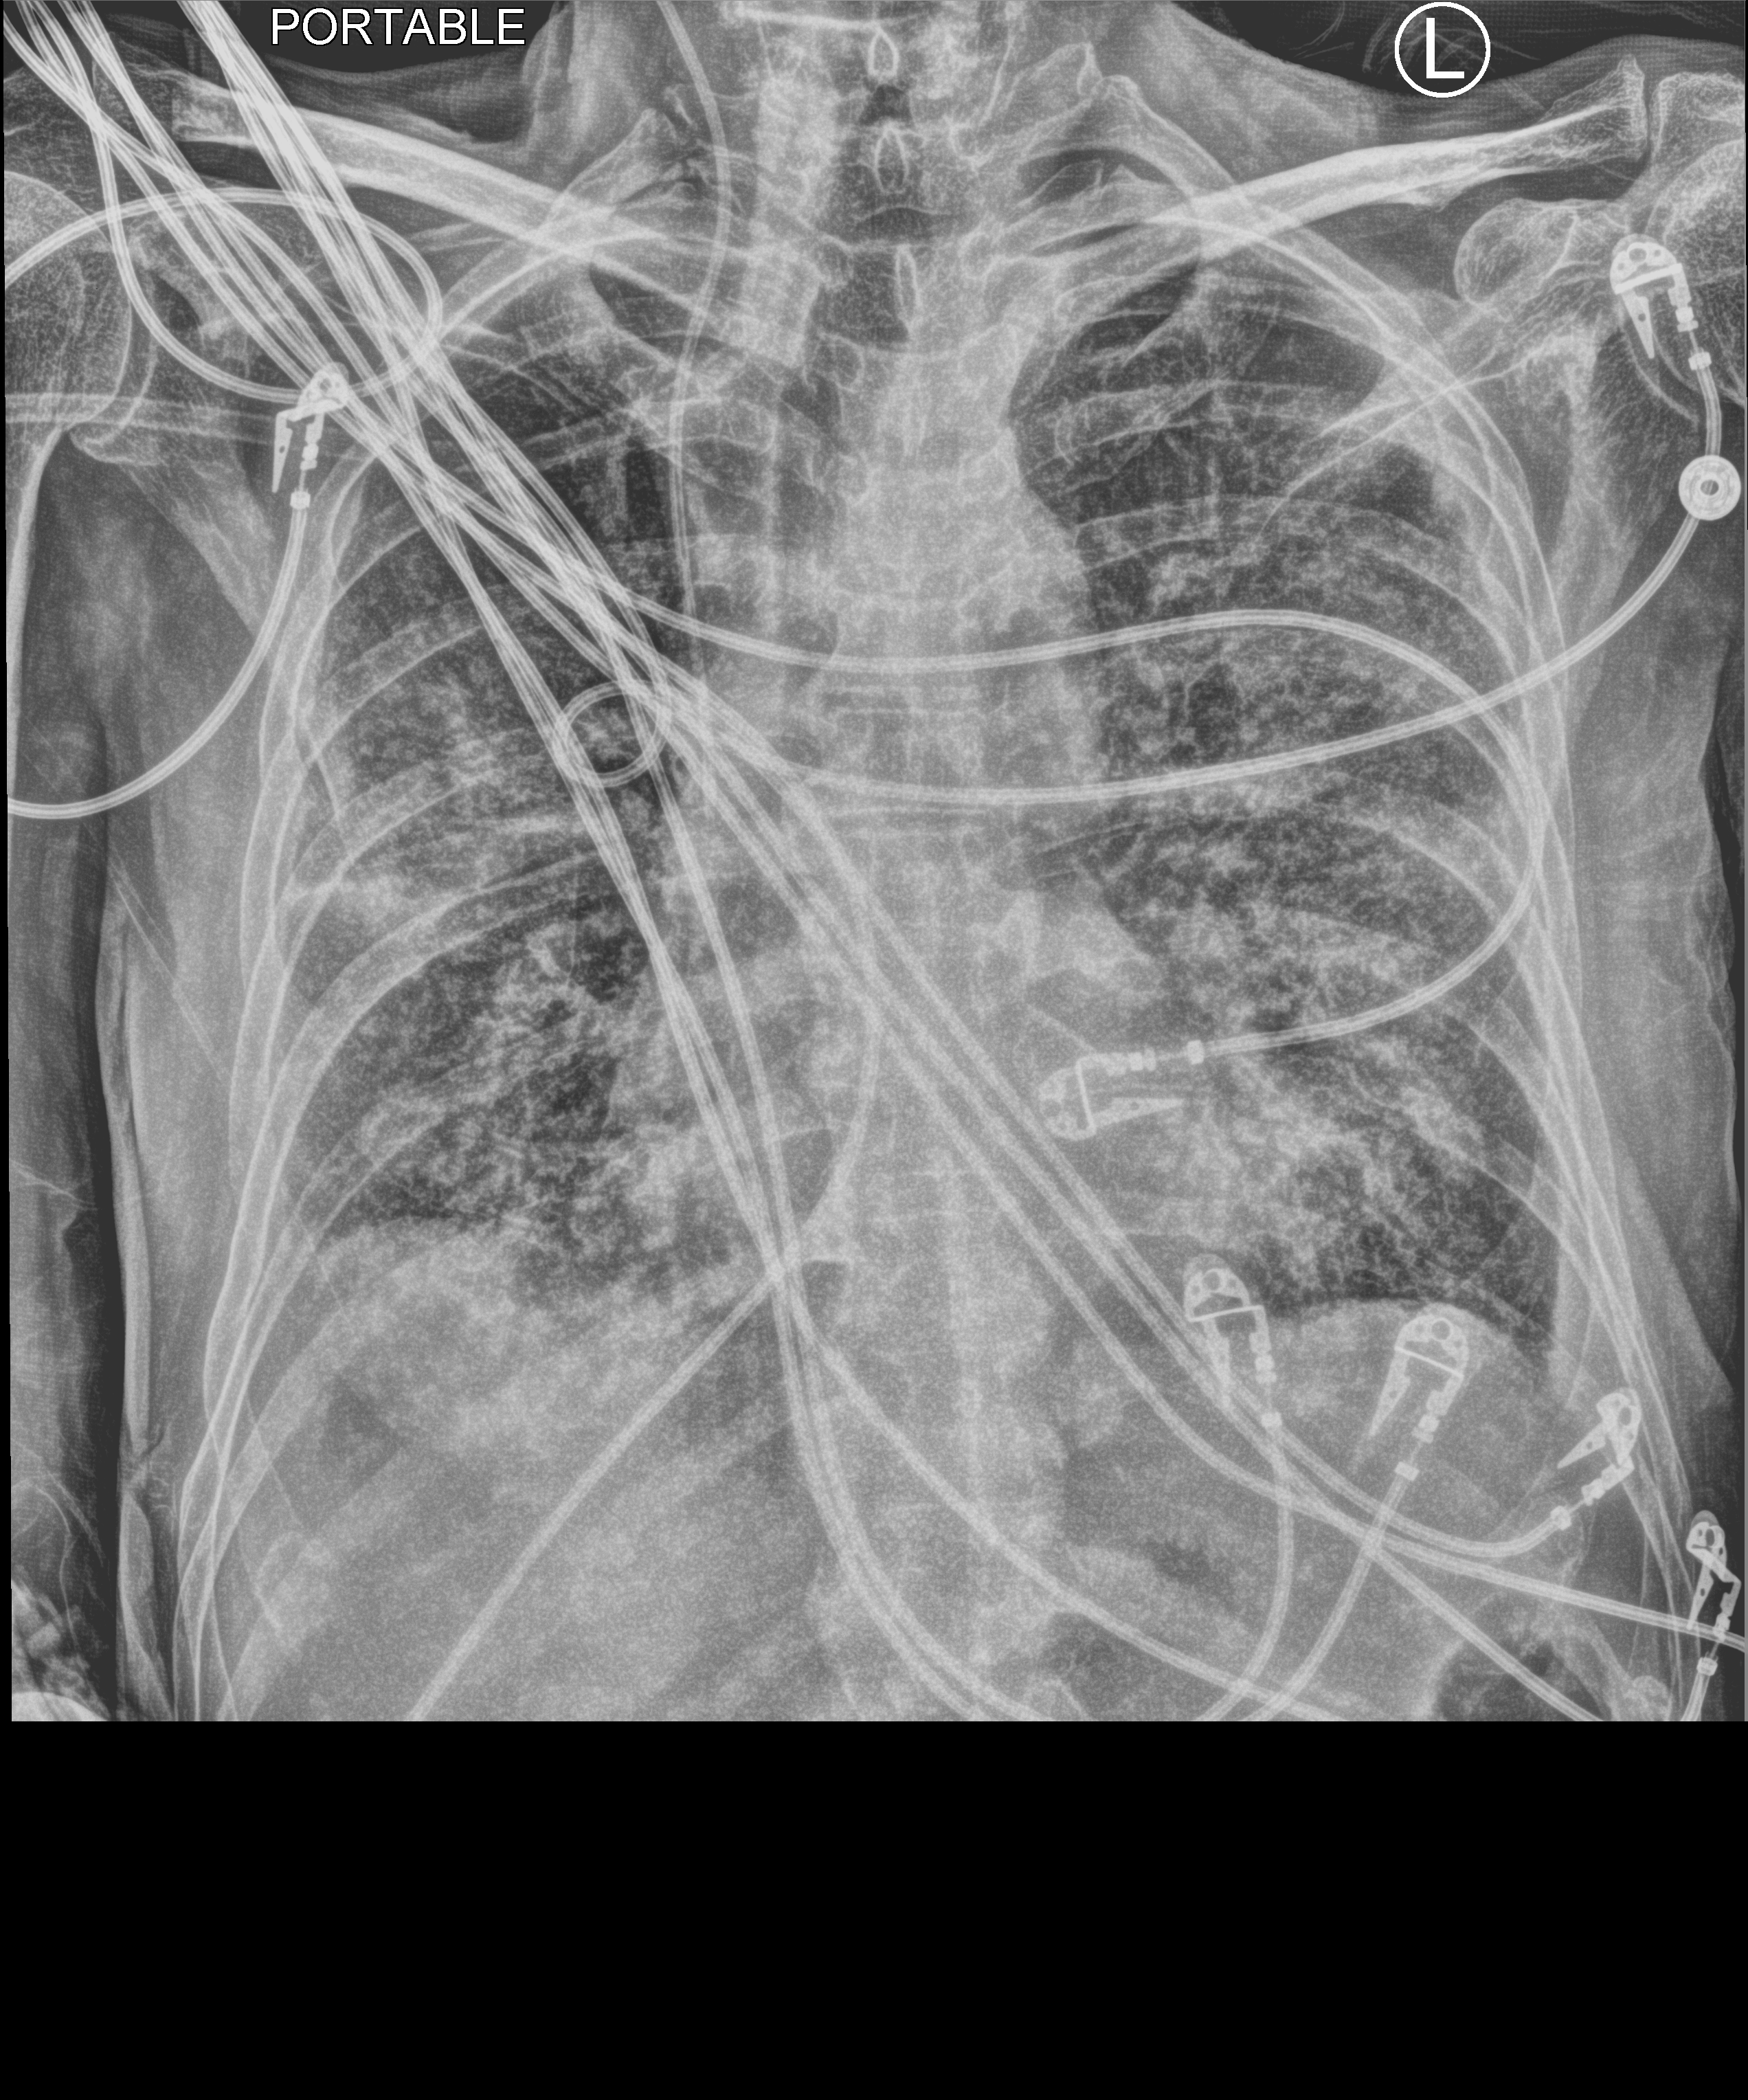
Bedside chest radiograph (computed radiography); anteroposterior (AP) projection. Male patient hospitalised with COVID-19, age 60–74 years.
Hospital-stay facts (about this admission, not read from this image; timing relative to this image not recorded): other chronic lung disease (admission record): no; admitted to intensive care during this hospital stay: yes.